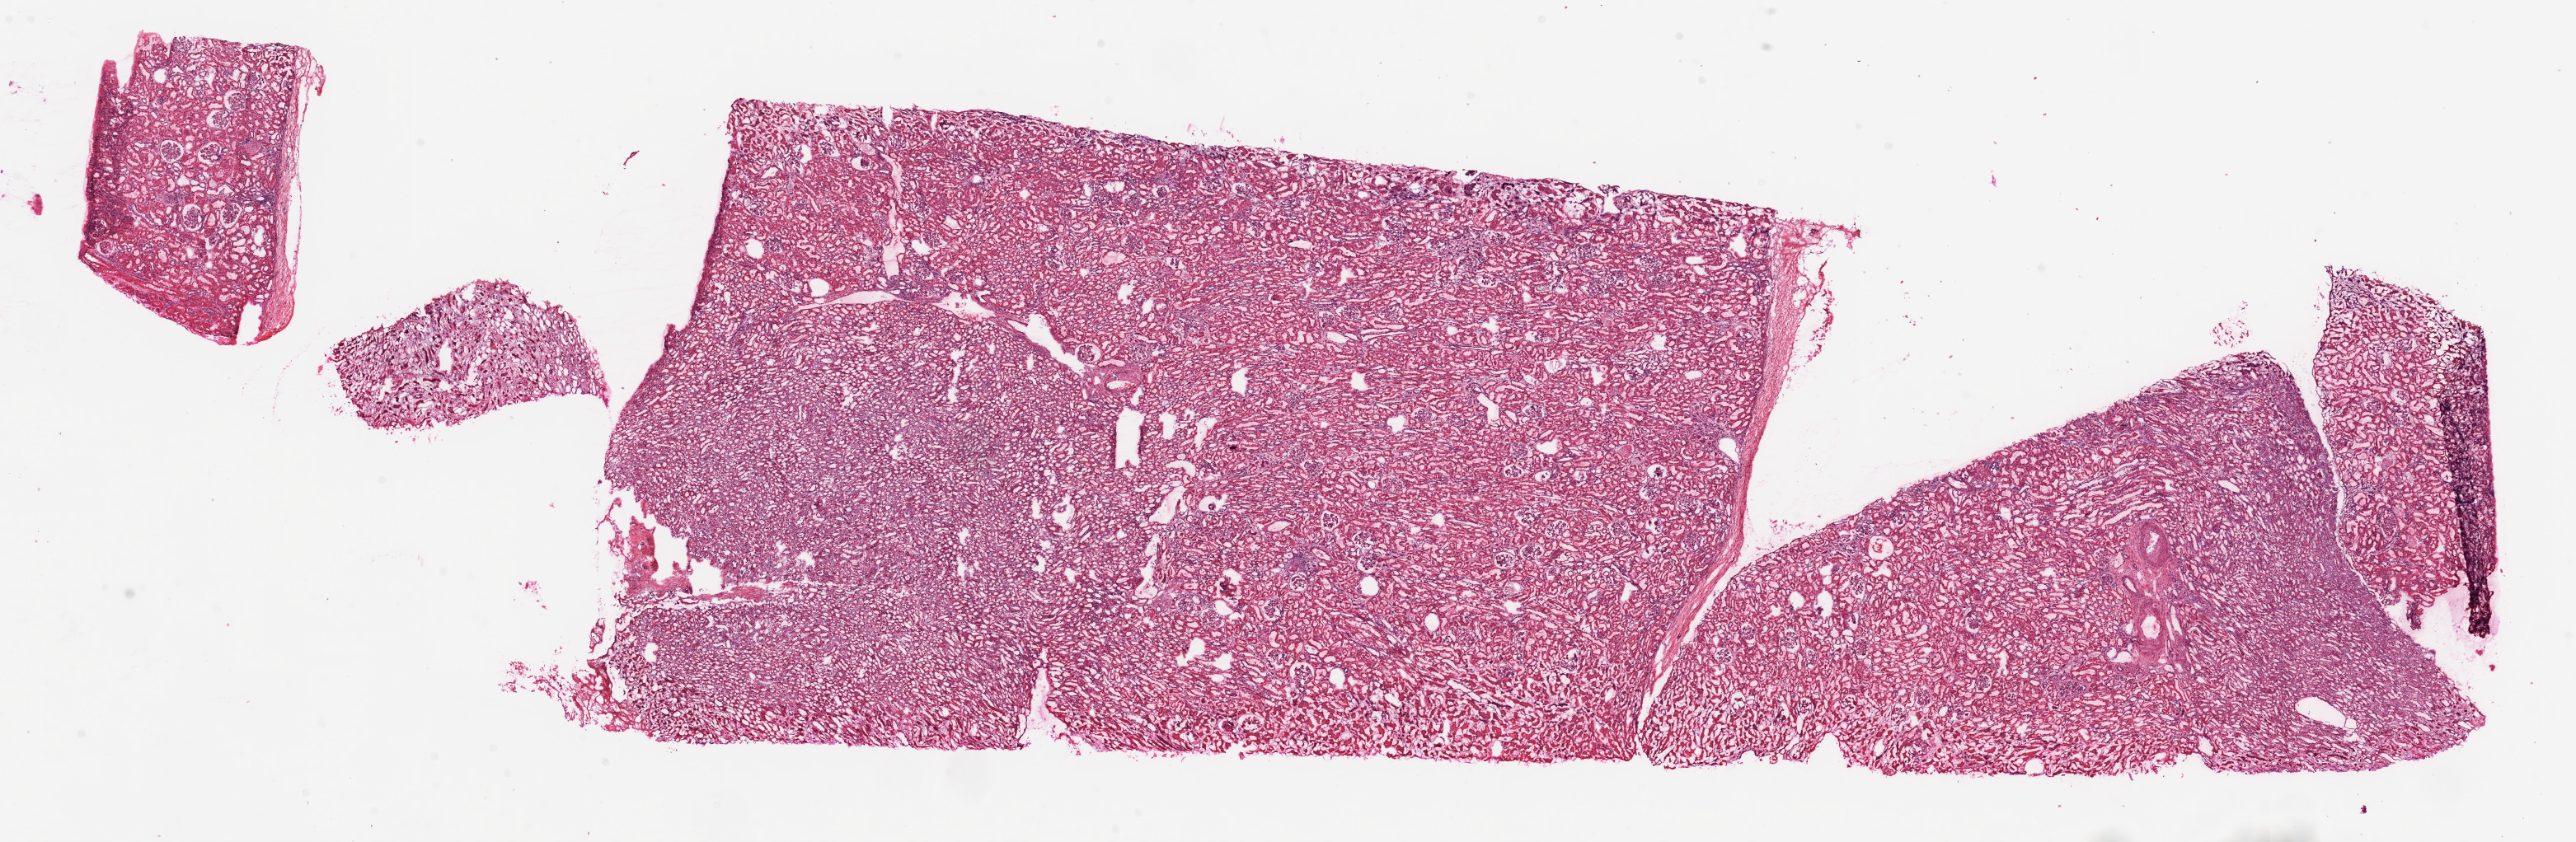
Hematoxylin and eosin (H&E) stained whole-slide image — a low-resolution overview of the entire scanned area, about 25.1 x 8.2 mm (acquisition: 20x scan), frozen section from the top of the tissue portion, solid tissue normal (non-tumour tissue) sample from the kidney. Patient: female, age at initial diagnosis 62 years.
This section: solid tissue normal (non-tumour) sample from the same patient. Patient diagnosis: Clear cell adenocarcinoma, NOS.